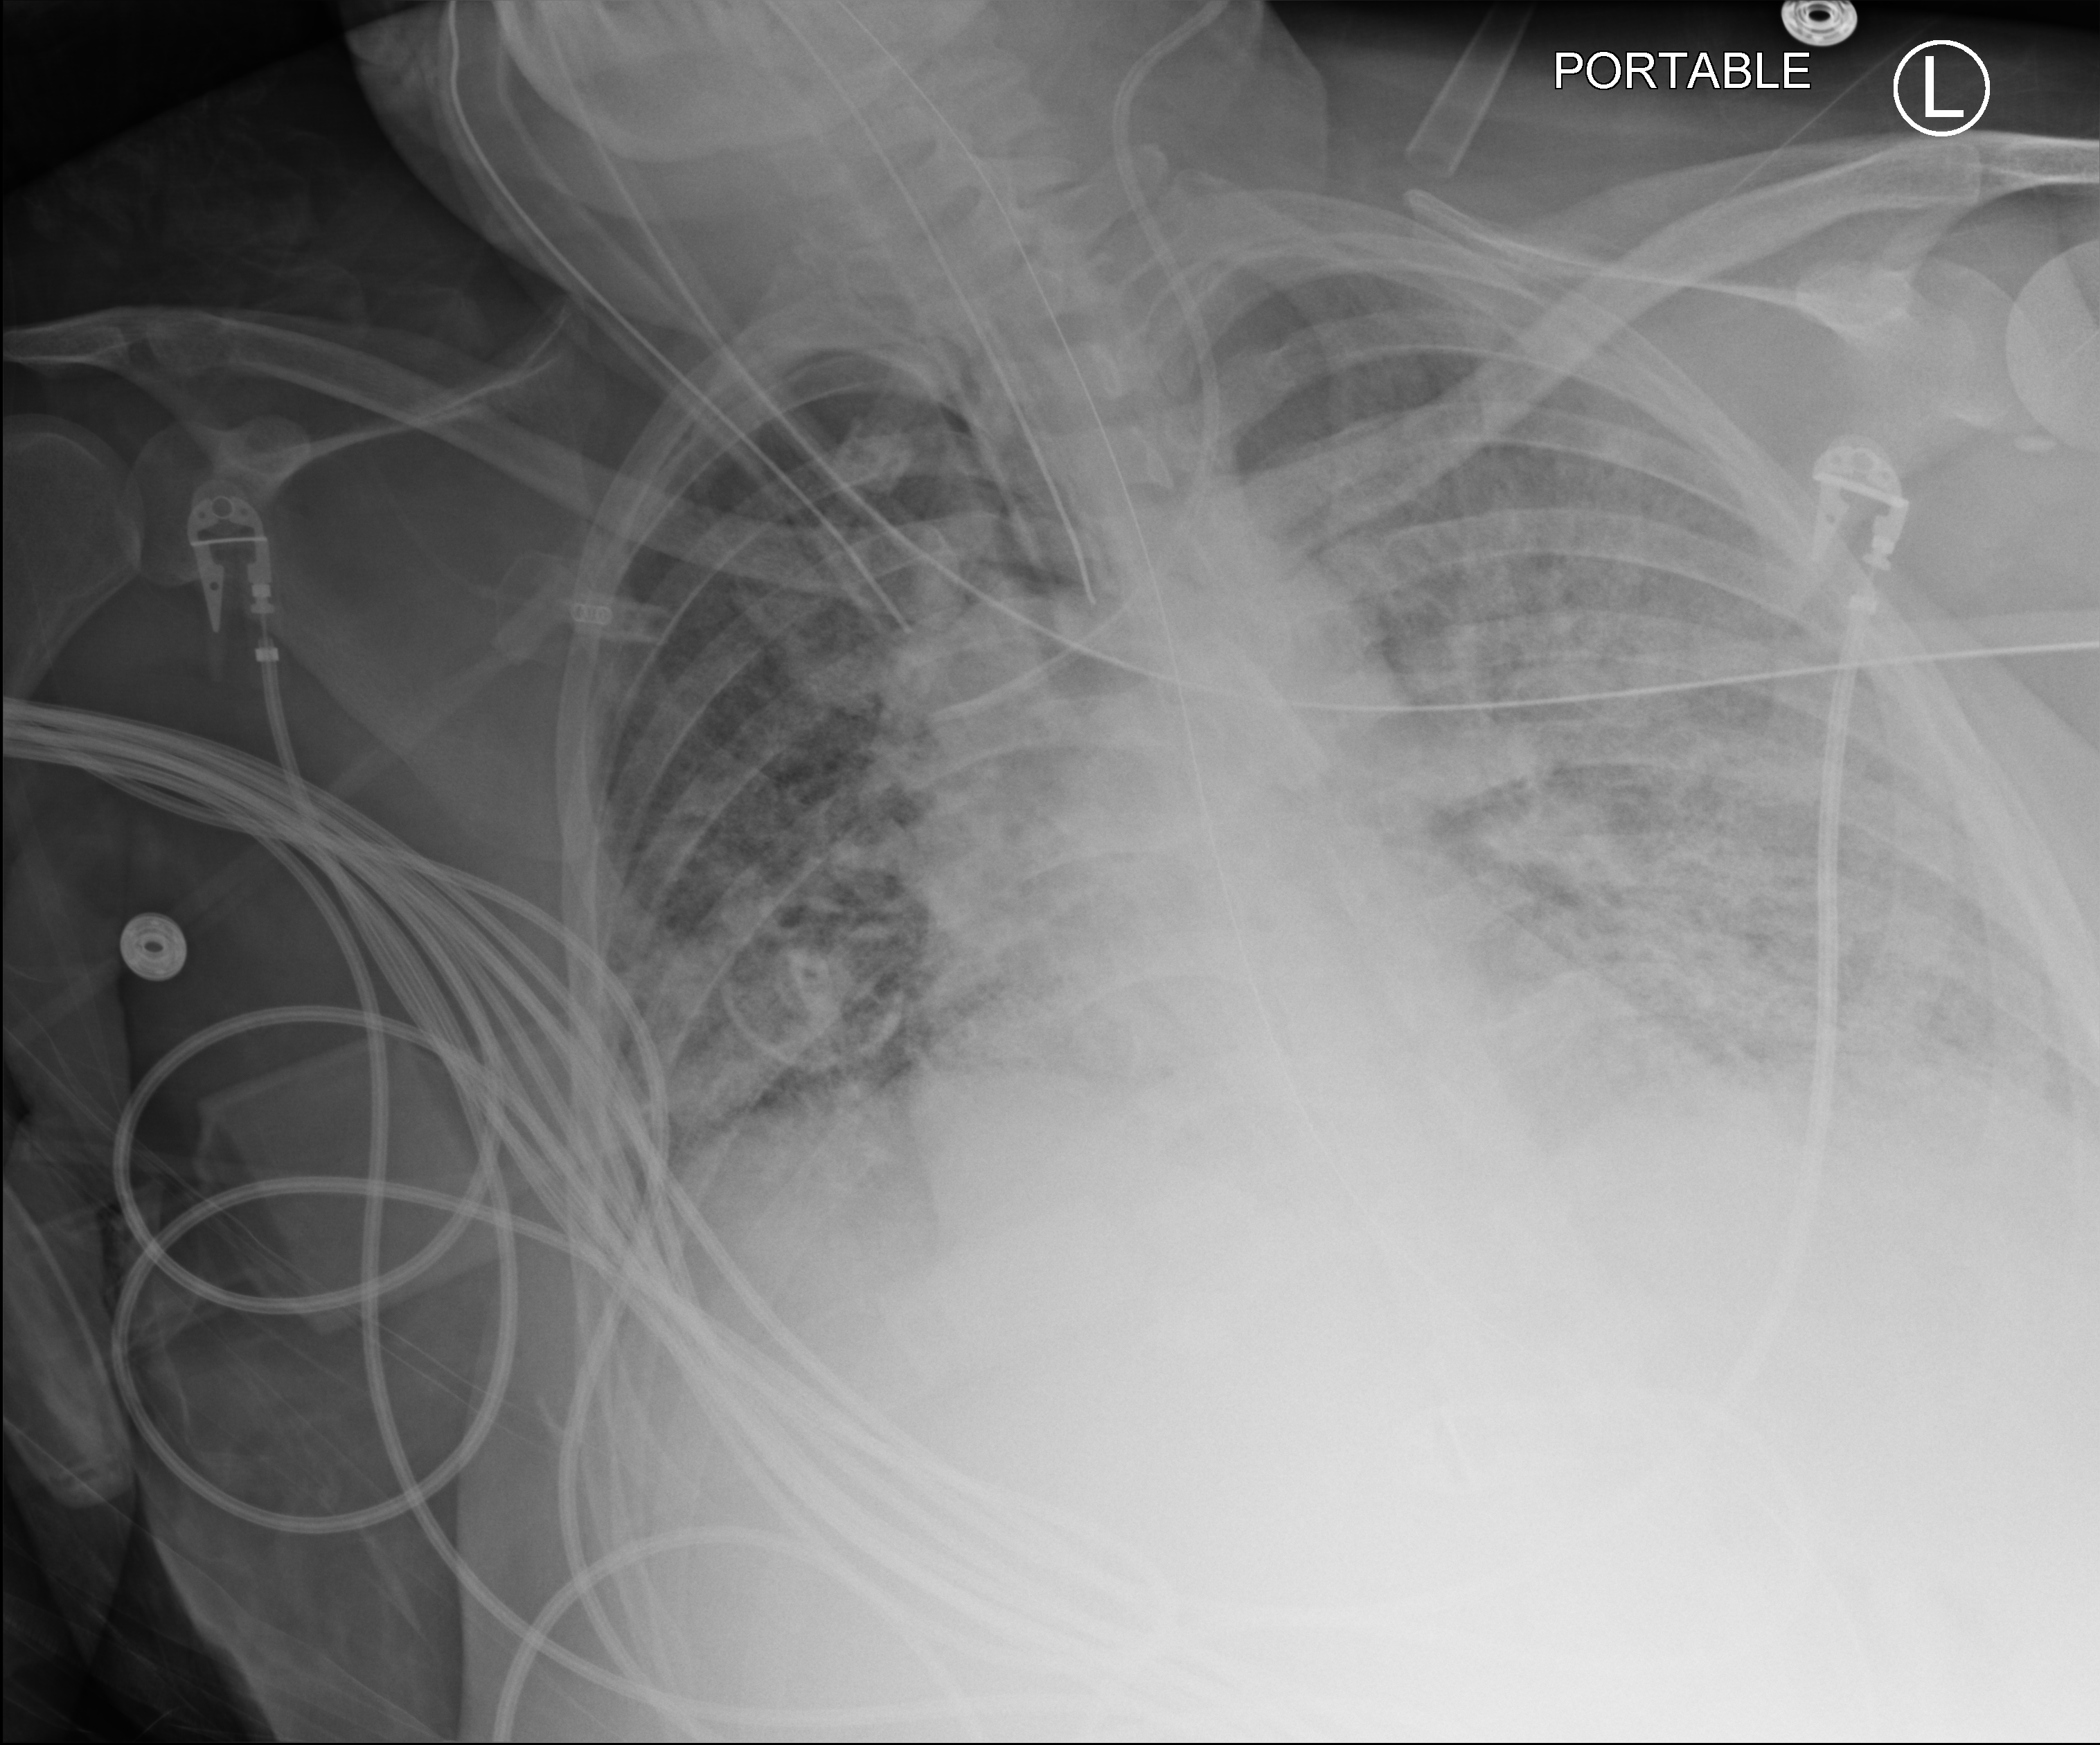
Portable chest radiograph. Patient hospitalised with COVID-19; female, aged 18–59 years.
From the hospital-stay record, not from the radiograph (when in the stay this image was taken is not recorded): admitted to intensive care during this hospital stay: no; mechanically ventilated during this hospital stay: yes.